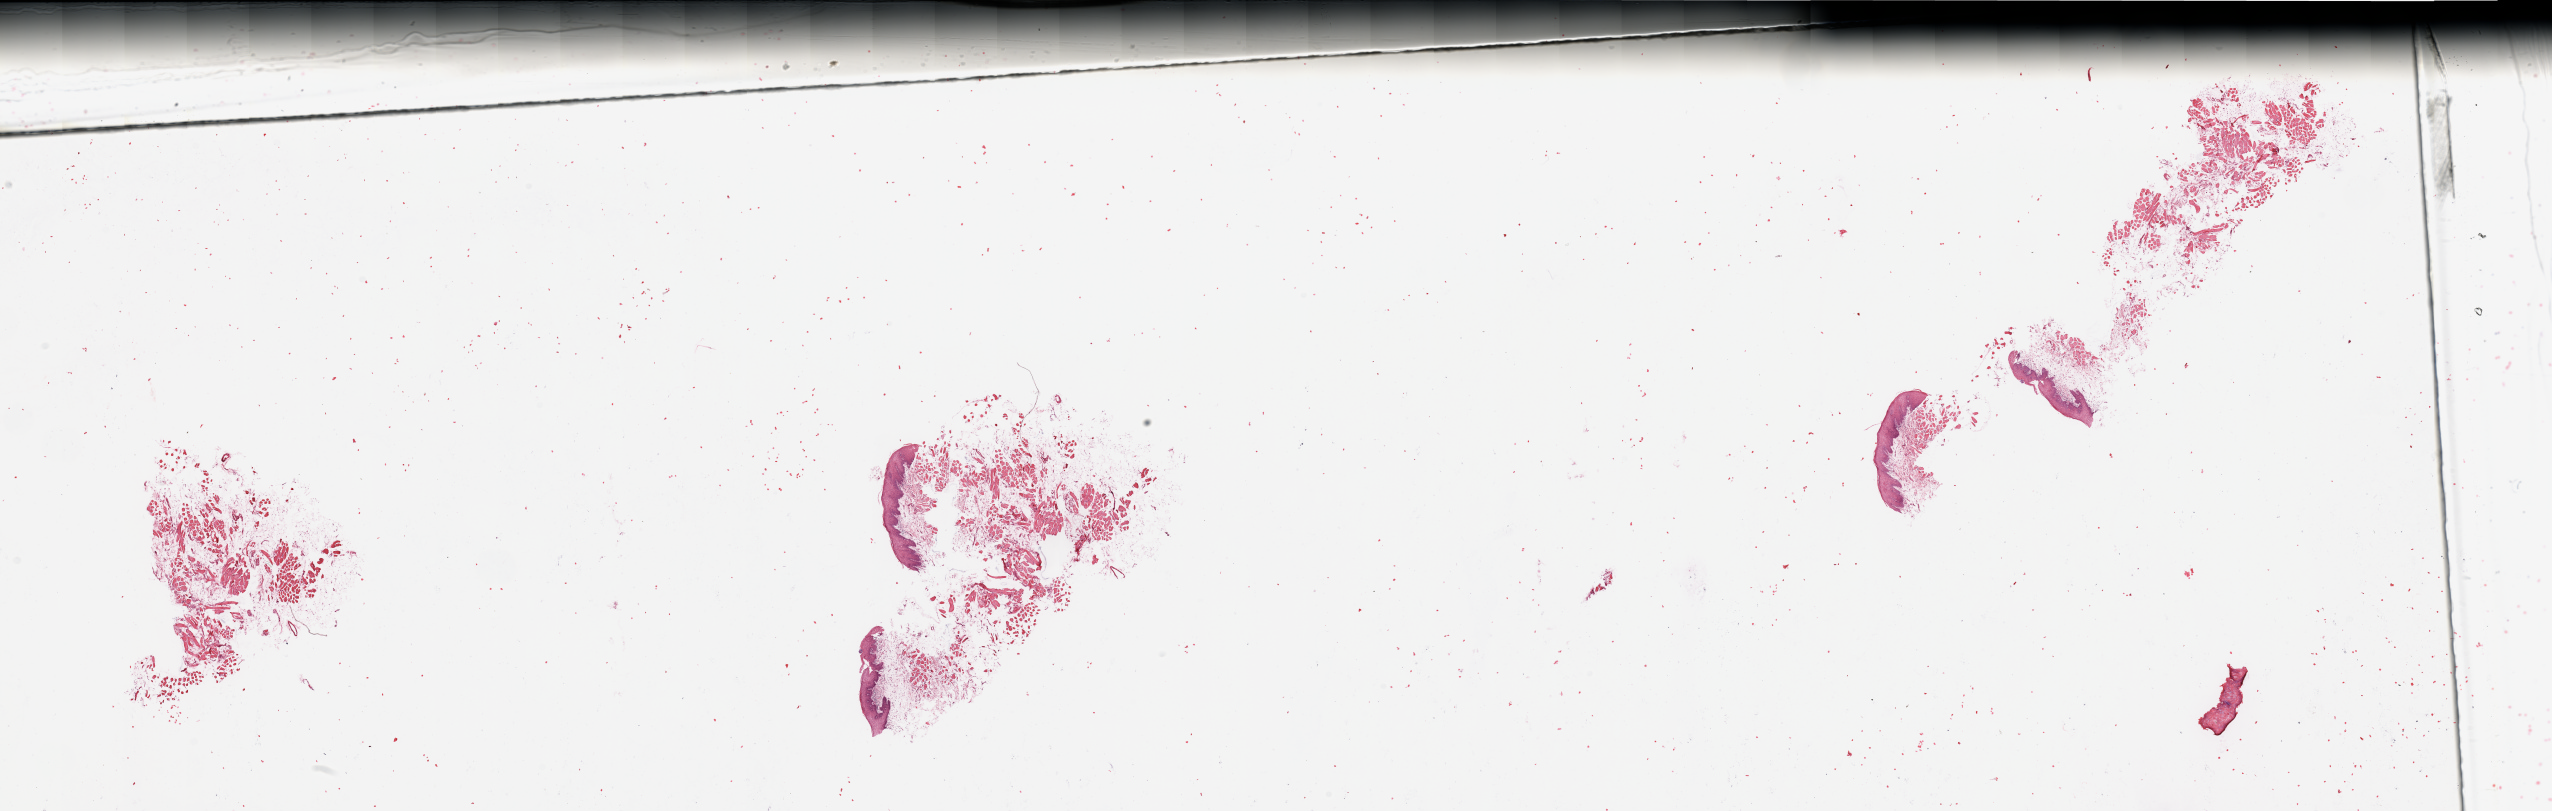
Whole-slide histology image, H&E, low-resolution overview of the scanned area, about 40.4 x 12.8 mm (acquisition: 20x scan). Normal (non-tumour) tissue sample, sampled site: tongue. 65-year-old male patient.
- this section: normal (non-tumour) tissue from the same patient
- patient diagnosis: Squamous cell carcinoma, NOS (tongue, NOS)